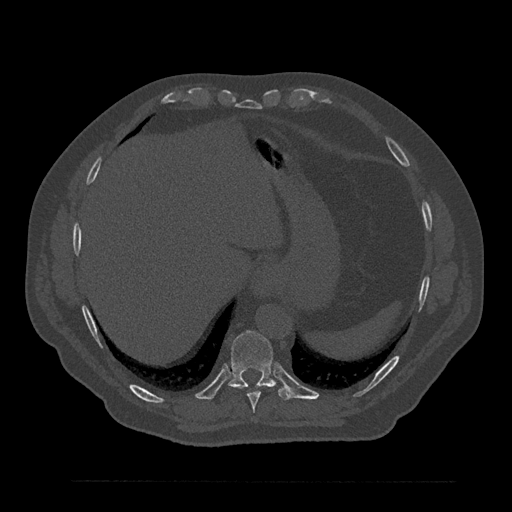
CT including the spine, one axial slice; slice 374 of 797 in the series (ordered by position); 120 kVp; bone window (W 1800 / L 400 HU); 0.5 mm slice thickness; 512 × 512 image matrix, field of view 430 × 430 mm. Male patient, age 61 years. From the clinical record (not read from this slice): primary cancer: prostate.
Outlined on this slice (semi-automatically segmented with operator editing):
- T10 vertebra: box from (x=228, y=331) to (x=290, y=400) px
- T9 vertebra: (x=237, y=384)–(x=267, y=413)